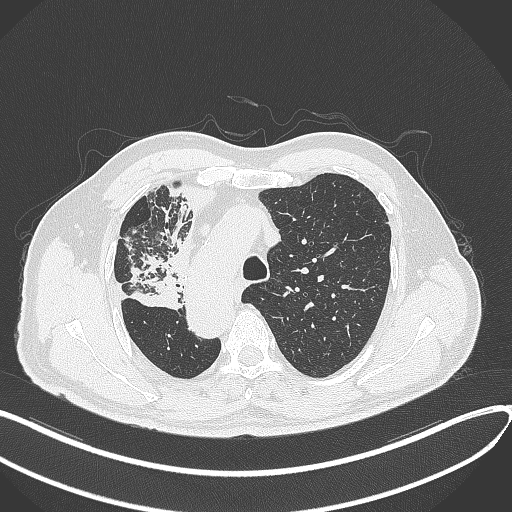
Chest CT, one axial slice. Slice 237 of 300 in the series (ordered by position). Reconstruction kernel B70f. Lung window (W 1500 / L -600 HU). 512 × 512 image matrix. Patient: male, 67 years. Case-level facts recorded for this patient, not image findings: clinical TNM (as recorded): T2a N0 M0.
Annotated regions visible in this slice (rectangle marked by the reading radiologist):
- lung tumour (recorded histology: squamous cell carcinoma): bounding box [x1, y1, x2, y2] px = [126, 246, 183, 313]